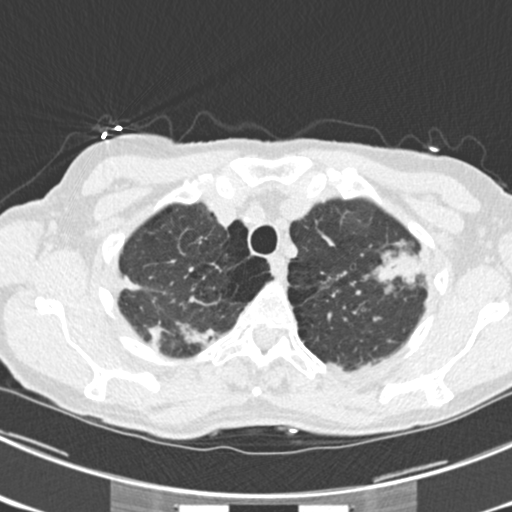
Low-dose screening chest CT, one axial slice; reconstruction kernel B30f; 120 kVp; lung window (W 1500 / L -600 HU); 2 mm slice thickness; 512 × 512 image matrix, field of view 302 × 302 mm.
Annotated regions visible in this slice (manually delineated by an expert):
- lesion 1 (tumor, upper lobe of left lung): box from (x=377, y=252) to (x=422, y=283) px
- lesion 4 (tumor, upper lobe of right lung): (x=146, y=320)–(x=204, y=346)